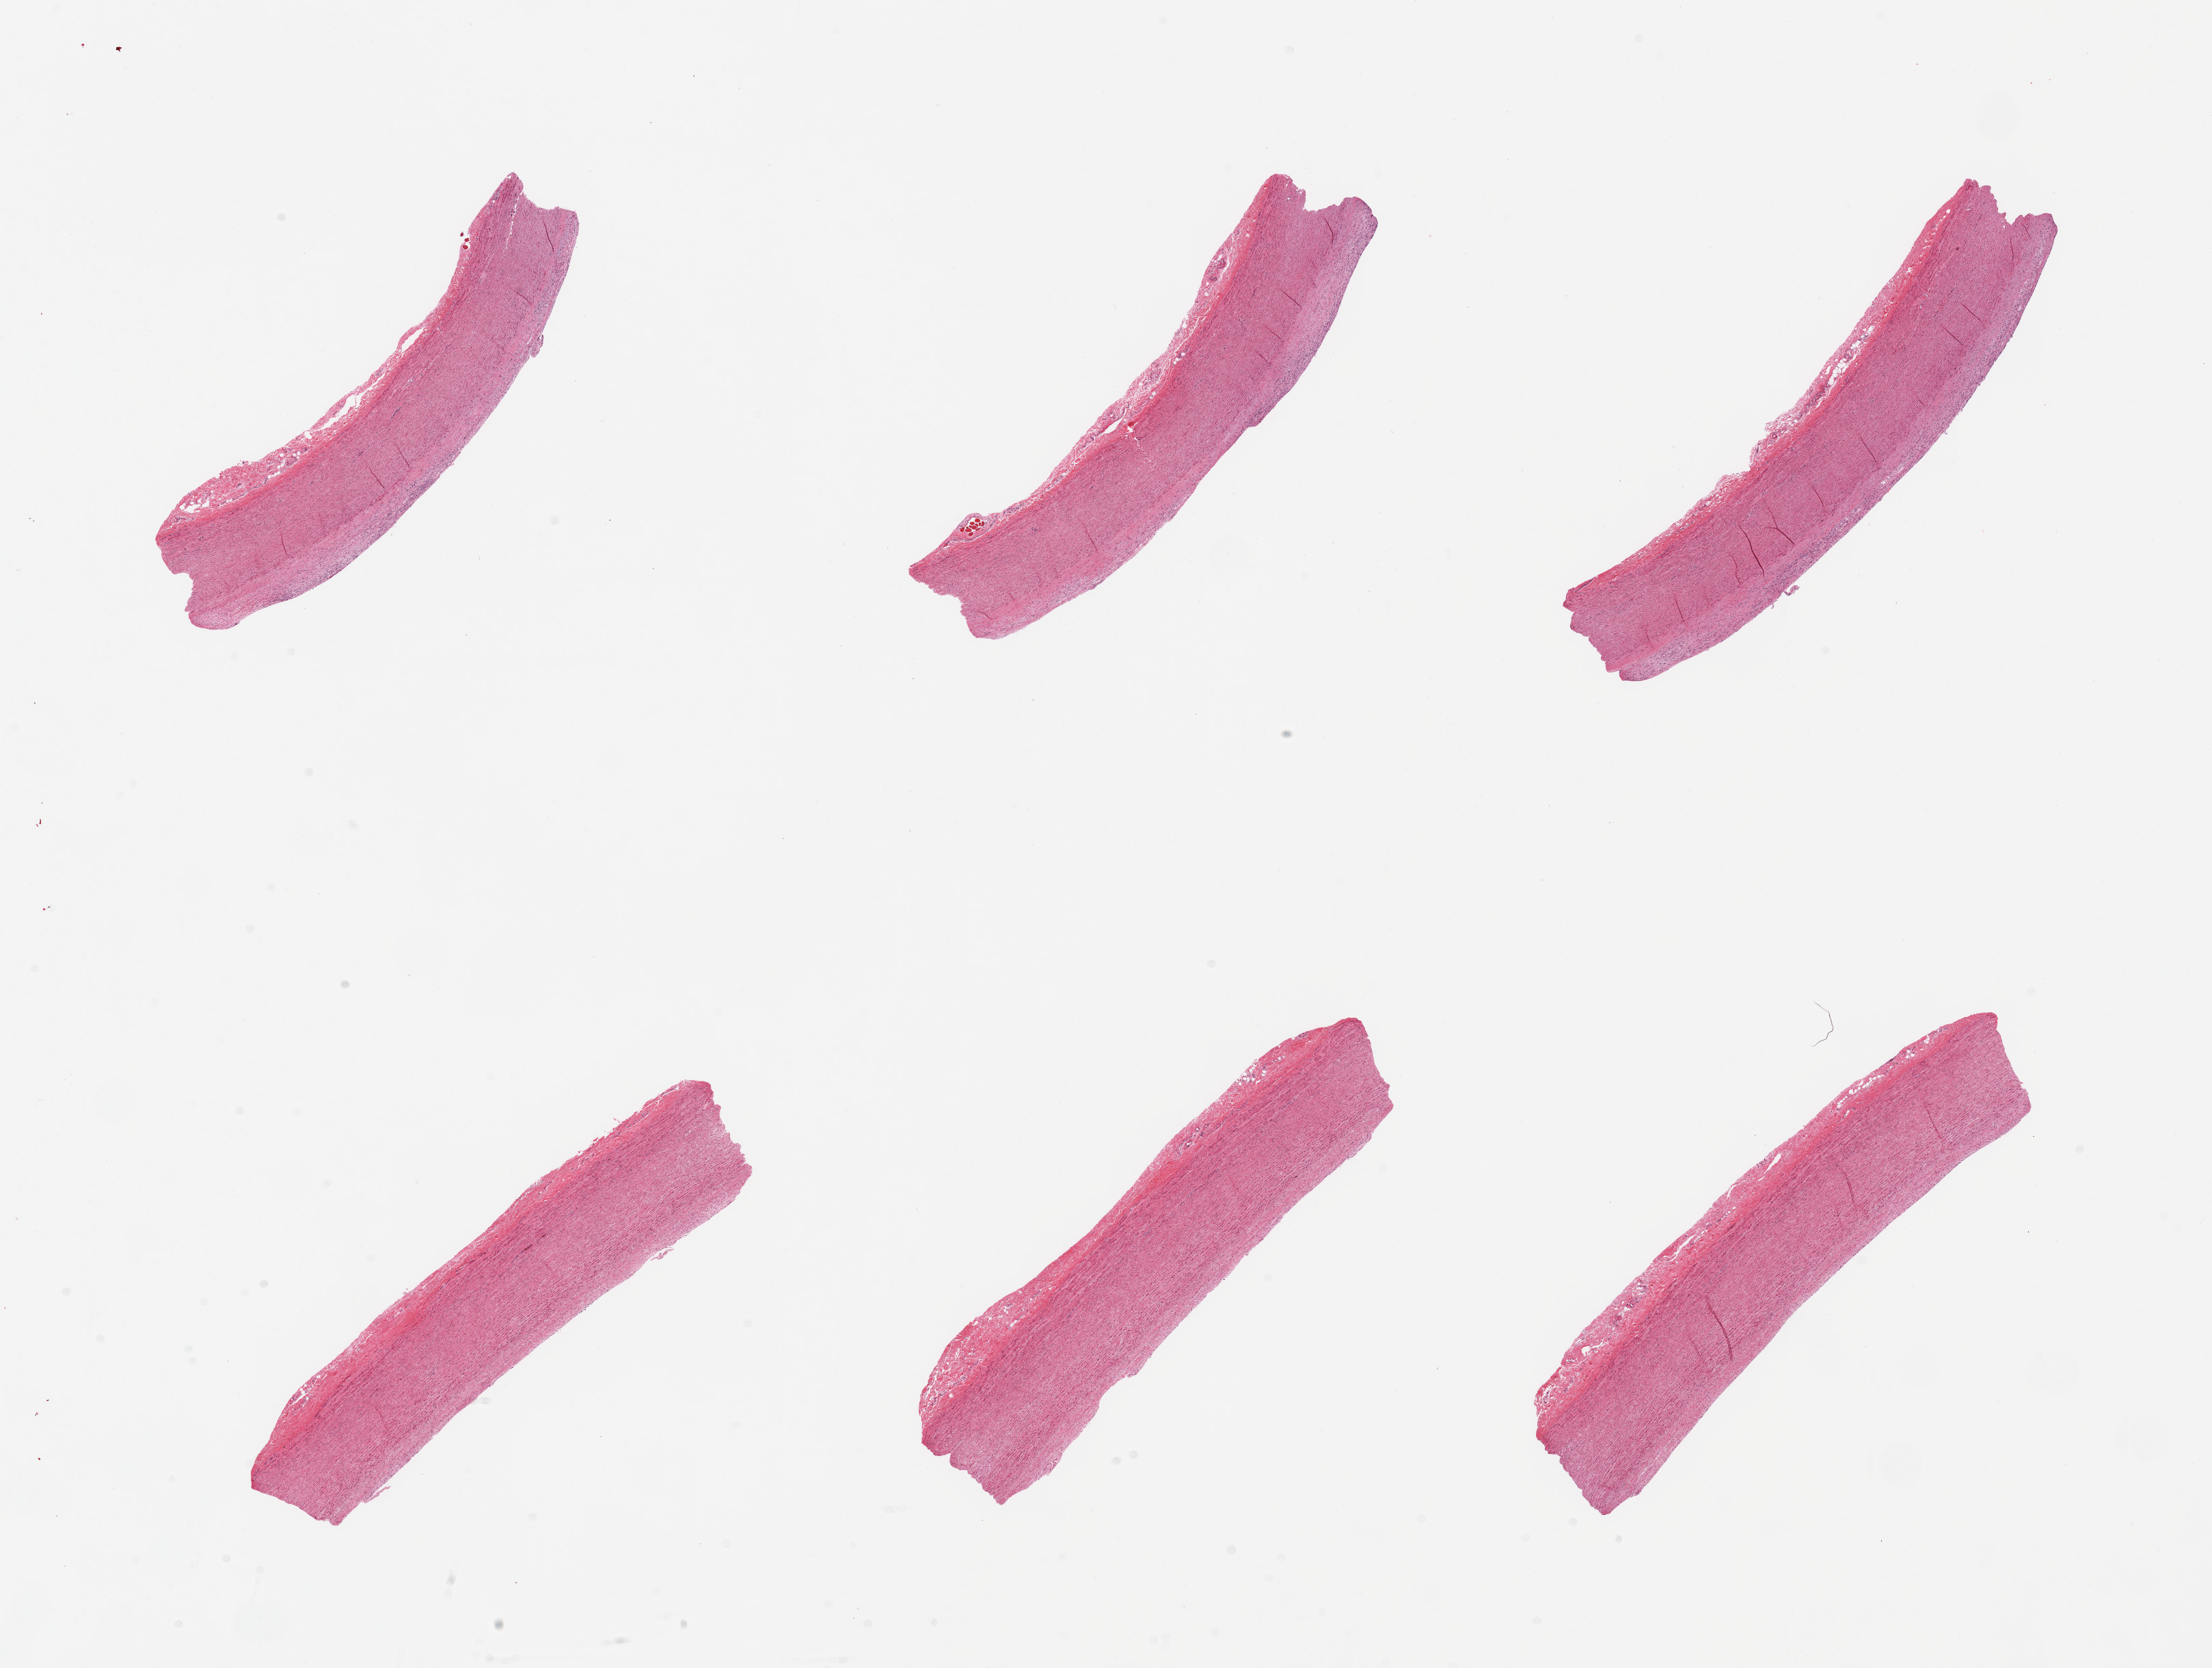
Whole-slide image, haematoxylin and eosin stain, low-resolution overview of the scanned area, about 25.6 x 19.3 mm (acquisition: 20x scan), PAXgene-fixed, paraffin-embedded tissue, section of aorta (target tissue), donor tissue sample. Male donor.
Reviewer comment on this tissue sample: 6 pieces, atherosis up to ~0.4mm.